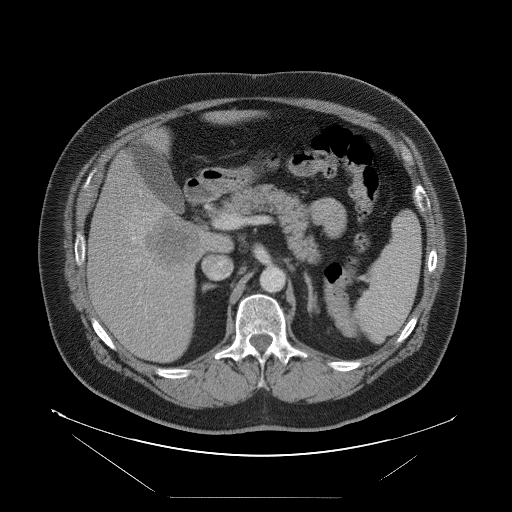
Contrast-enhanced abdominal CT, one axial slice; position 52 of 114 along the scan axis; 120 kVp; soft-tissue window (W 400 / L 40 HU); 5 mm slice thickness; 512 × 512 image matrix, field of view 500 × 500 mm. Male patient, age 61 years. Case-level facts recorded for this patient, not image findings: diagnosis: colorectal cancer liver metastases, imaged before liver resection; multiple liver metastases: no; largest metastasis: 6.5 cm; chemotherapy before resection: no.
Annotated regions visible in this slice (manually delineated by an expert):
- hepatic veins: bounding box <132,237,135,240> (left, top, right, bottom; pixels)
- liver: <89,111,247,362>
- planned liver remnant (the part of the liver to remain after resection): <140,112,249,151>
- liver metastasis: <147,214,196,270>